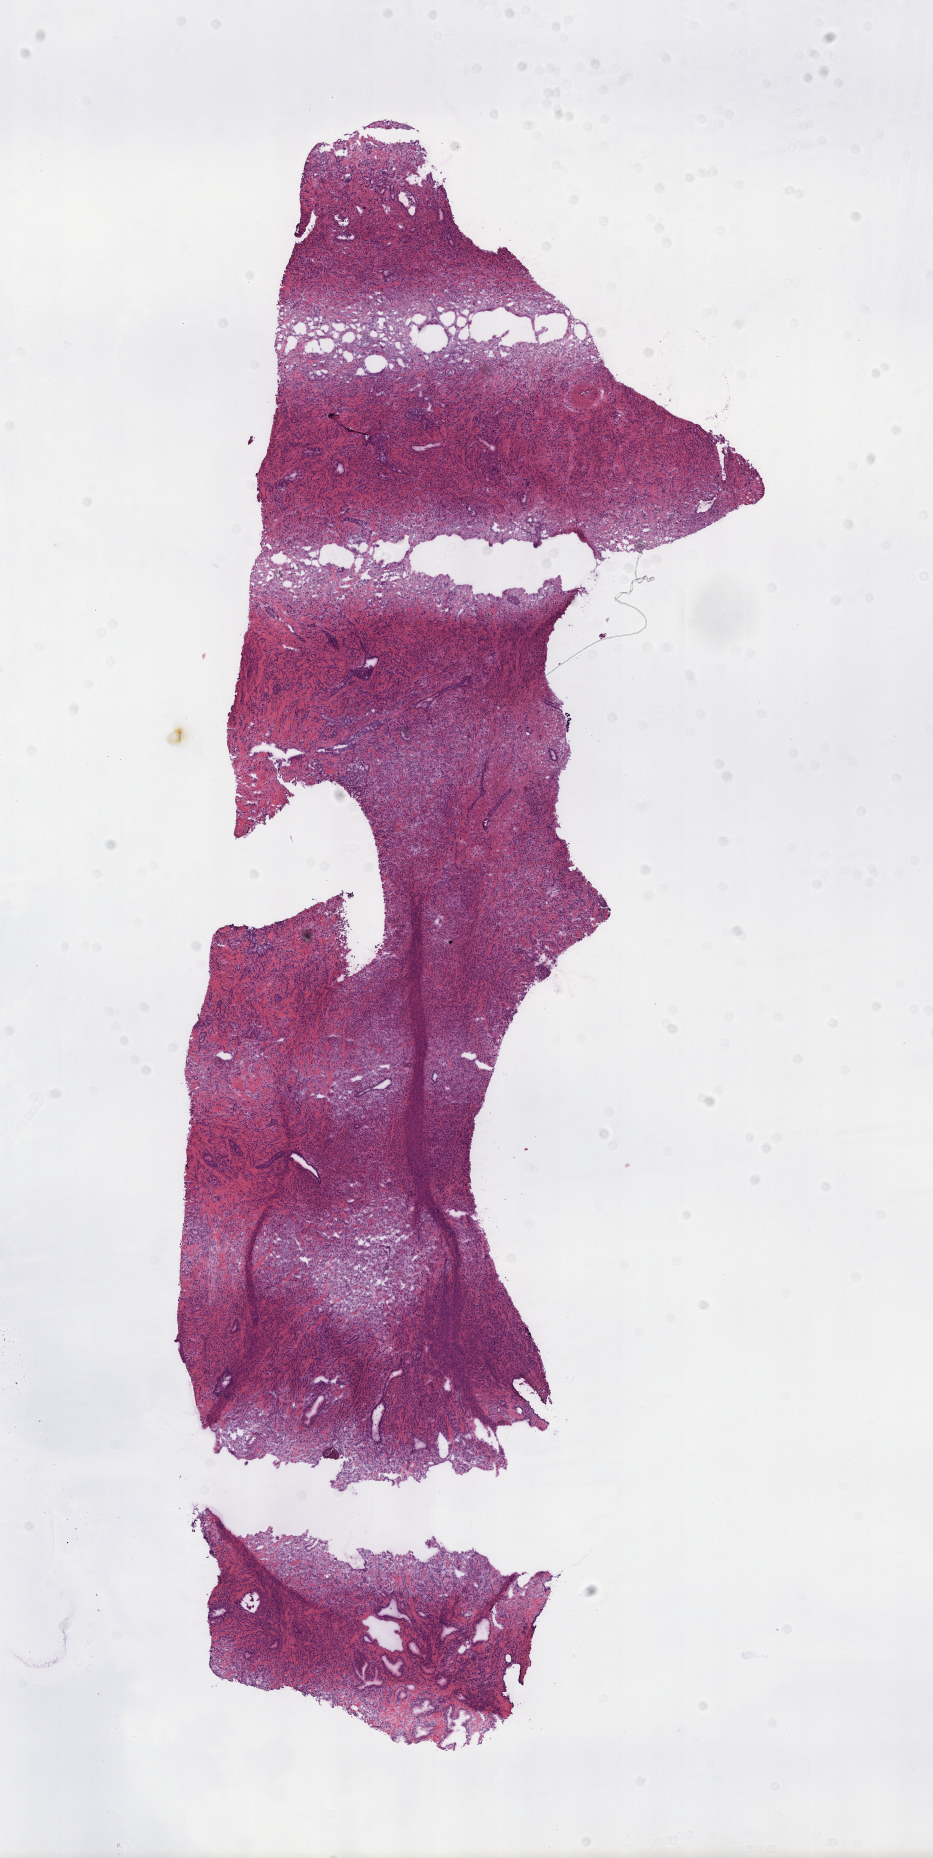
H&E-stained whole-slide image, whole scanned area (about 7.6 x 15.0 mm, from a 40x scan) shown as a low-resolution overview. Frozen section from the top of the tissue portion. Prostate, primary tumour sample. Patient: male, age at initial diagnosis 61 years. Gleason score: 9 (4+5). Pathologist review of this section (percent, as recorded): tumour cells 100%, tumour nuclei 90%, normal cells 0%, stromal cells 0%, necrosis 0%. Infiltration values recorded for this section: lymphocyte infiltration 0%, monocyte infiltration 0%, neutrophil infiltration 0%.
Lymph nodes positive (case pathology): 1 of 8 examined. Diagnosis: Adenocarcinoma, NOS (prostate gland).